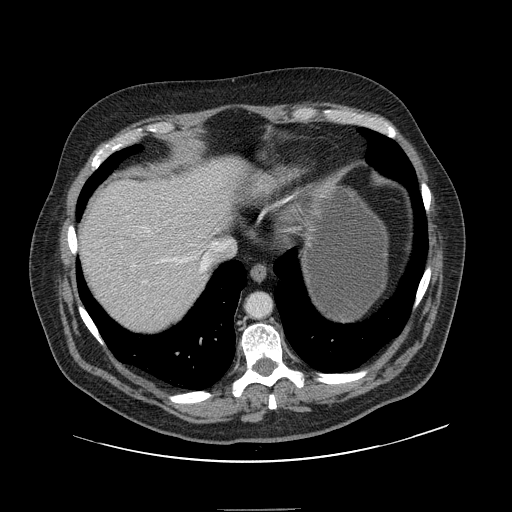
Contrast-enhanced abdominal CT, one axial slice; position 128 of 154 along the scan axis; intravenous contrast given; soft-tissue window (W 400 / L 40 HU); 2.5 mm slice thickness; 512 × 512 image matrix. Male patient, age 61 years. From the clinical record (not read from this slice): diagnosis: colorectal cancer liver metastases, imaged before liver resection; multiple liver metastases: yes; largest metastasis: 2.6 cm; chemotherapy before resection: no.
Annotated regions visible in this slice (manually delineated by an expert):
- hepatic veins: box from (x=161, y=242) to (x=215, y=272) px
- liver: (x=78, y=157)–(x=241, y=334)
- planned liver remnant (the part of the liver to remain after resection): (x=78, y=157)–(x=241, y=333)
- portal vein (with intrahepatic branches): (x=127, y=216)–(x=147, y=283)